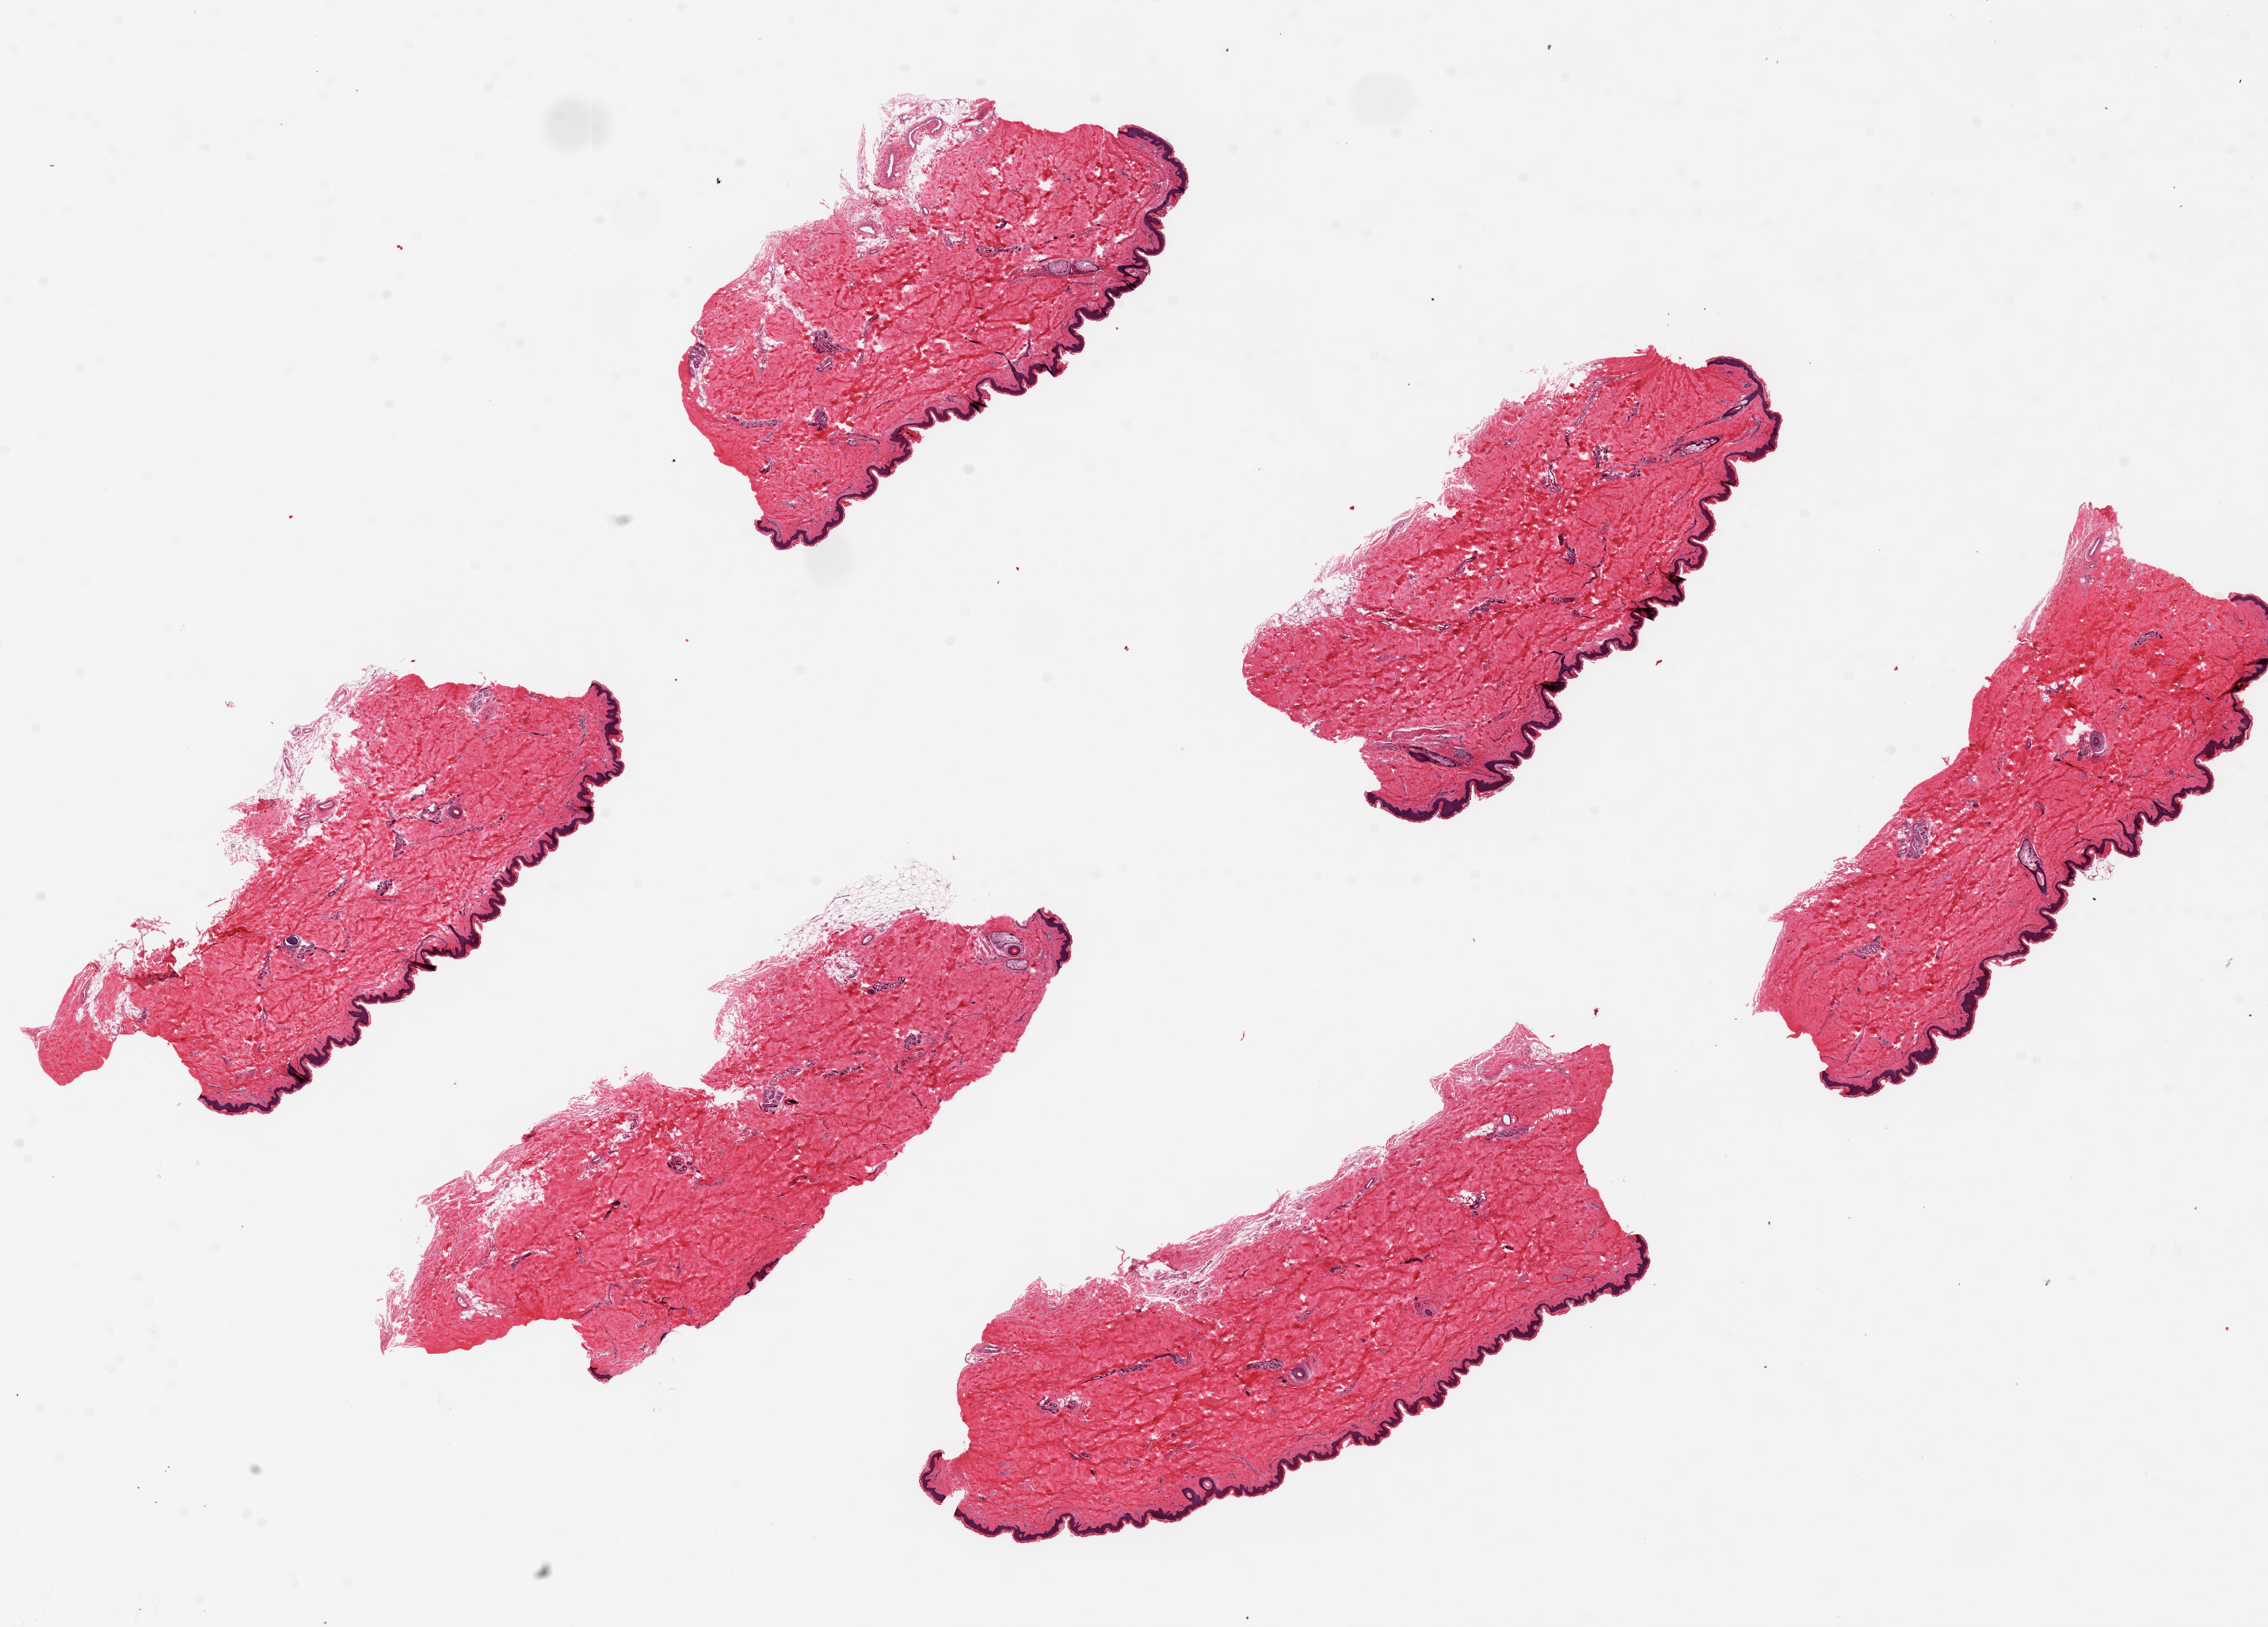
Haematoxylin and eosin whole-slide image, brightfield, whole scanned area (about 22.6 x 16.2 mm) shown as a low-resolution overview, PAXgene-fixed, paraffin-embedded tissue, sampled site (target tissue): skin of lower leg, donor tissue sample.
• pathologist's review note for this sample: 6 pieces ~5x2.5mm. Squamous epithelium is ~2-3% of thickness